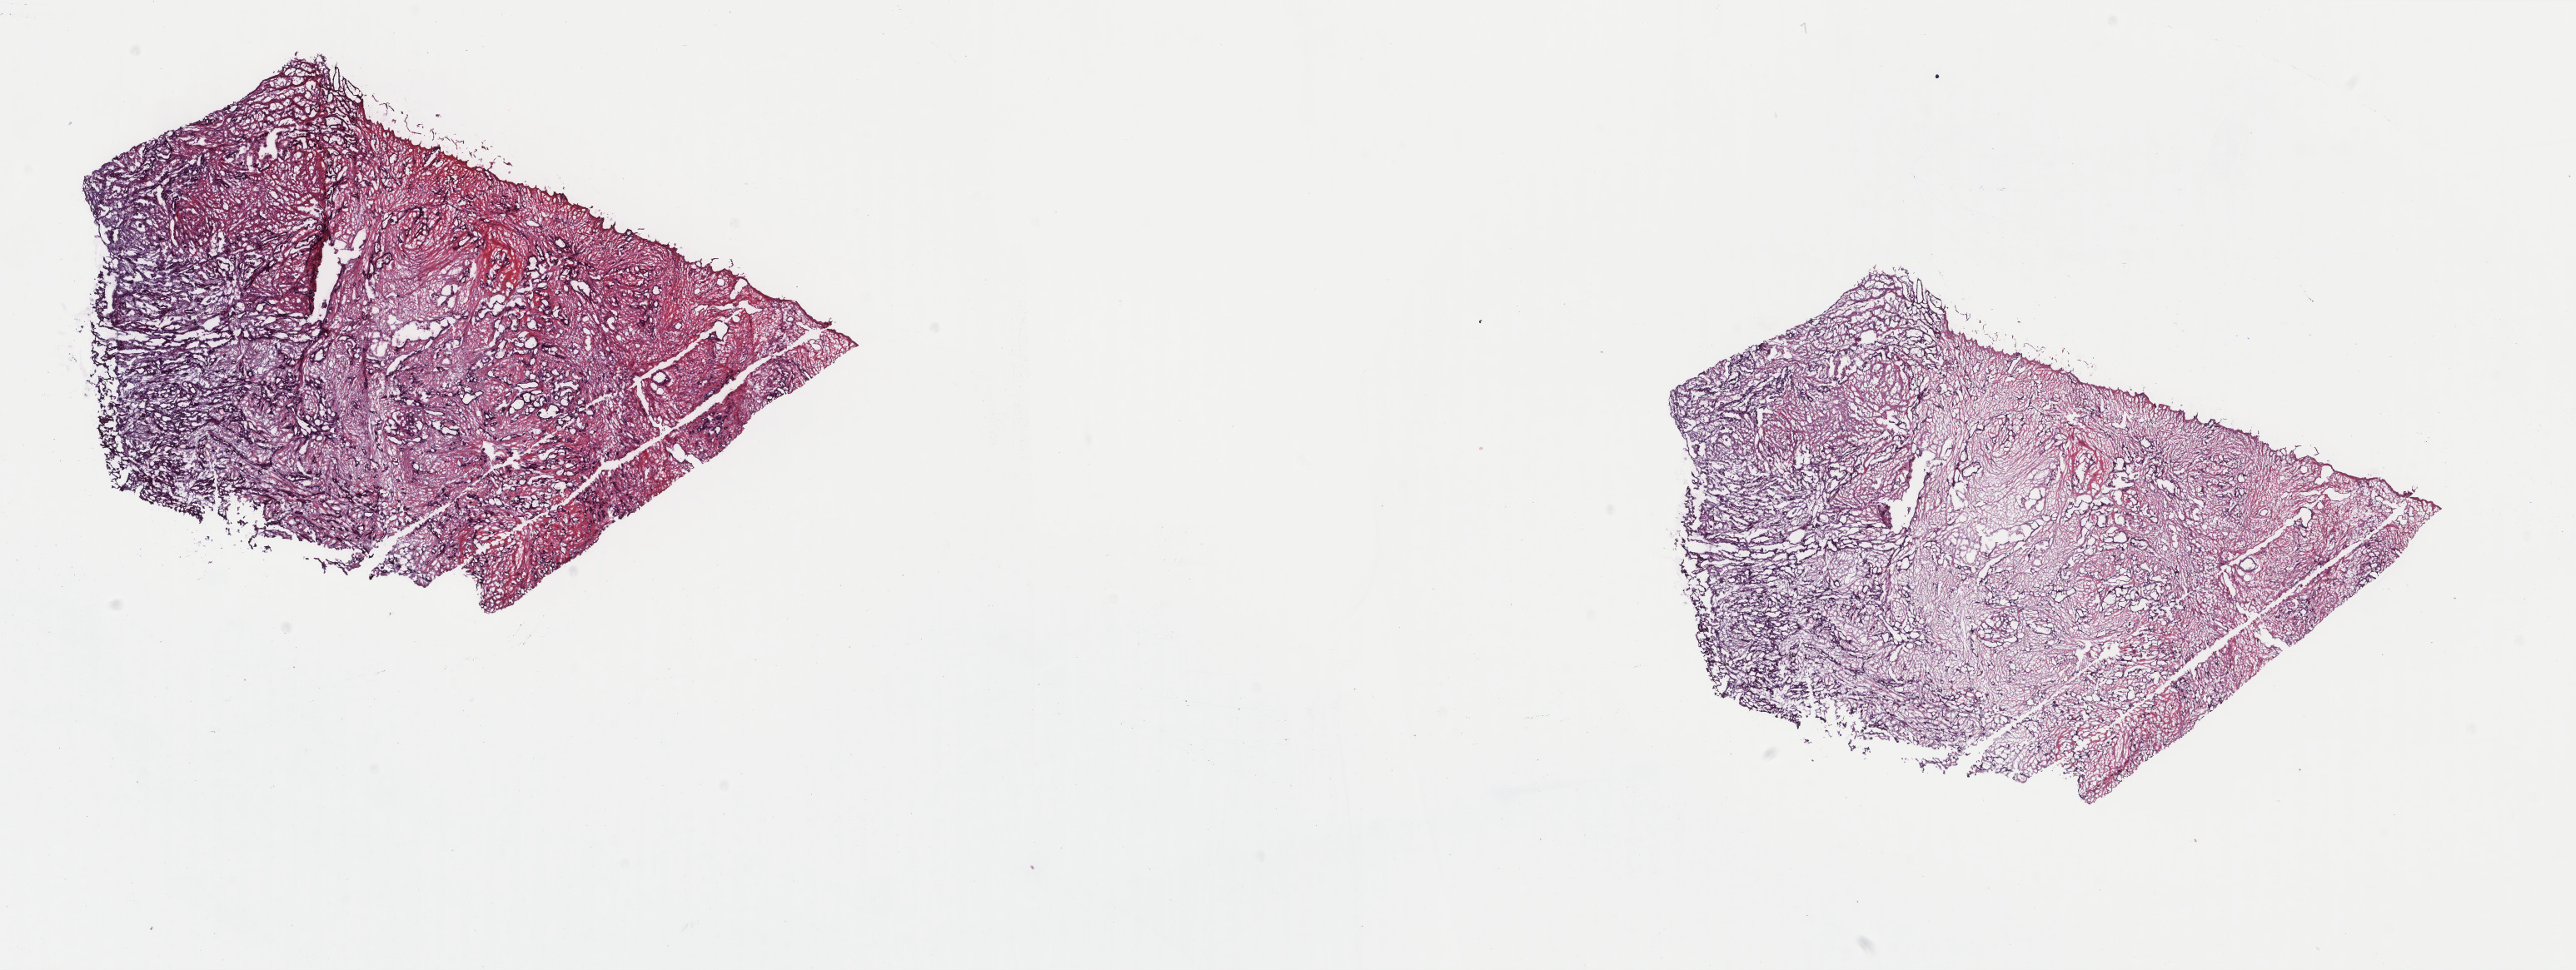
H&E-stained whole-slide image, low-resolution overview of the scanned area, about 24.6 x 9.2 mm (acquisition: 40x scan), frozen section from the top of the tissue portion, sample: primary tumour, stomach. Male patient; age at initial diagnosis 58 years. Histologic grade: G3 (poorly differentiated). Slide review estimates, as recorded: tumour cells 45%, tumour nuclei 75%, normal cells 0%, stromal cells 52%, necrosis 3%. Inflammatory infiltration, as recorded: lymphocyte infiltration 2%, monocyte infiltration 0%, neutrophil infiltration 0%.
TNM: T4a N1 M0. Diagnosis: Adenocarcinoma, NOS. AJCC pathologic stage: IIIA.